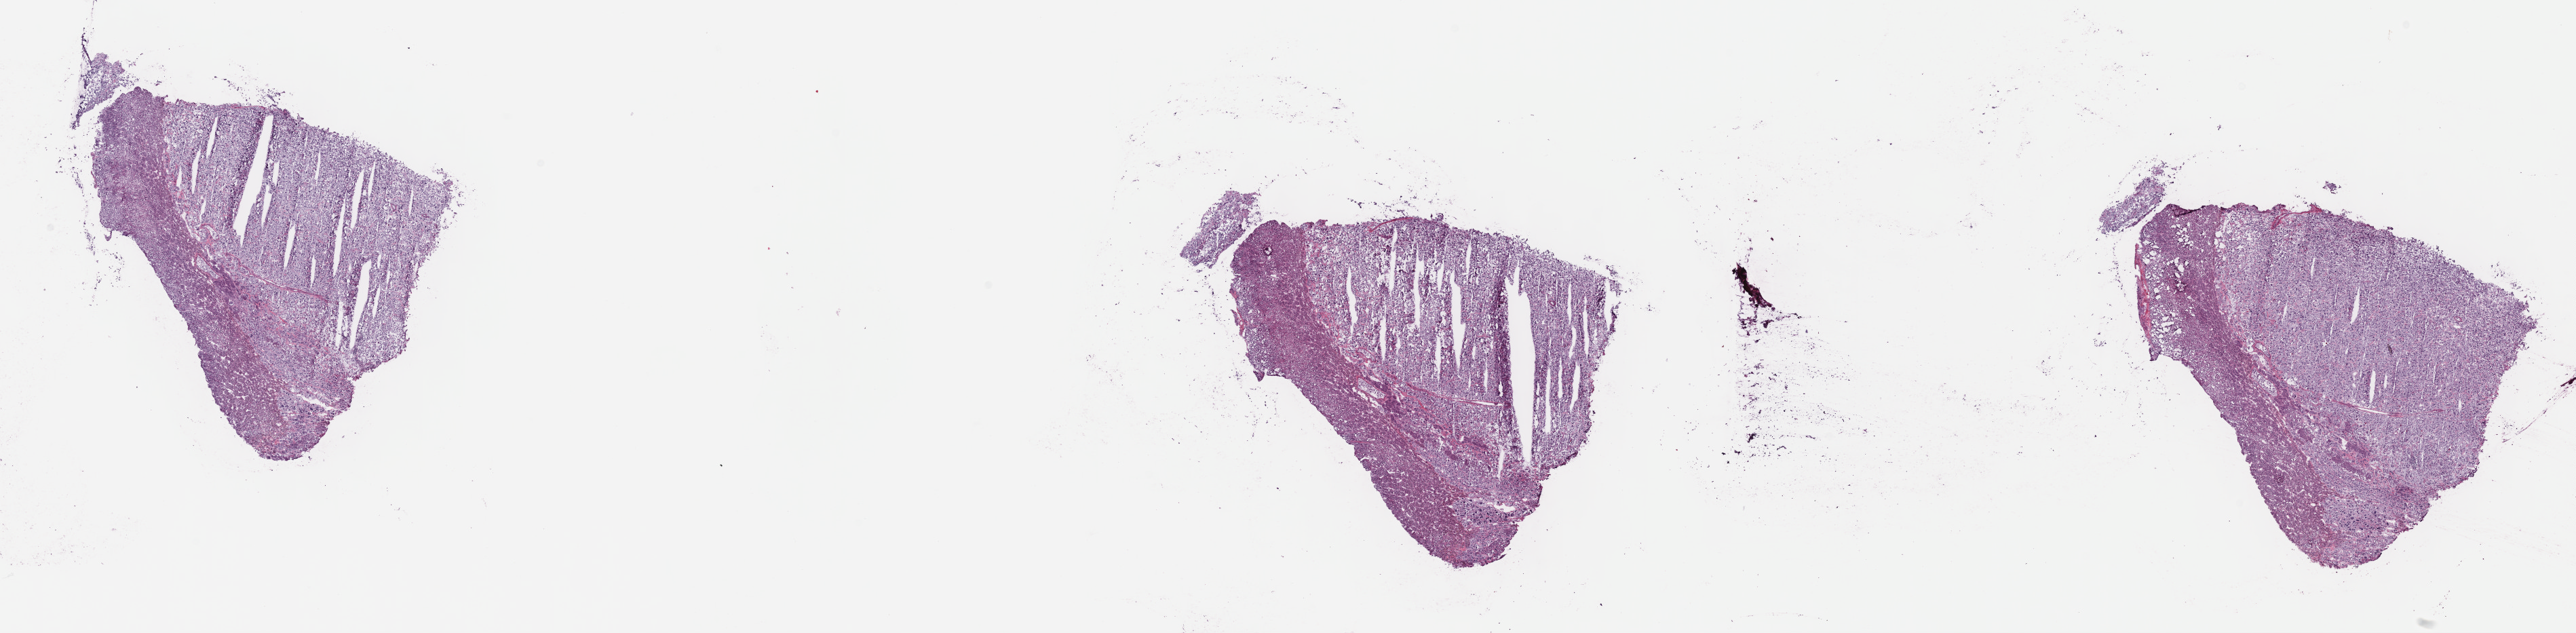
Digitized H&E-stained tissue section (whole slide) — whole scanned area (about 30.7 x 7.5 mm) shown as a low-resolution overview; frozen section; adrenal gland, primary tumour sample. Male patient; age at initial diagnosis 24 years. Slide review estimates, as recorded: tumour cells 70%, tumour nuclei 70%, normal cells 15%, stromal cells 15%, necrosis 0%. Inflammatory infiltration, as recorded: lymphocyte infiltration 1%, monocyte infiltration 1%, neutrophil infiltration 1%.
* diagnosis: Medullary carcinoma, NOS
* laterality: bilateral